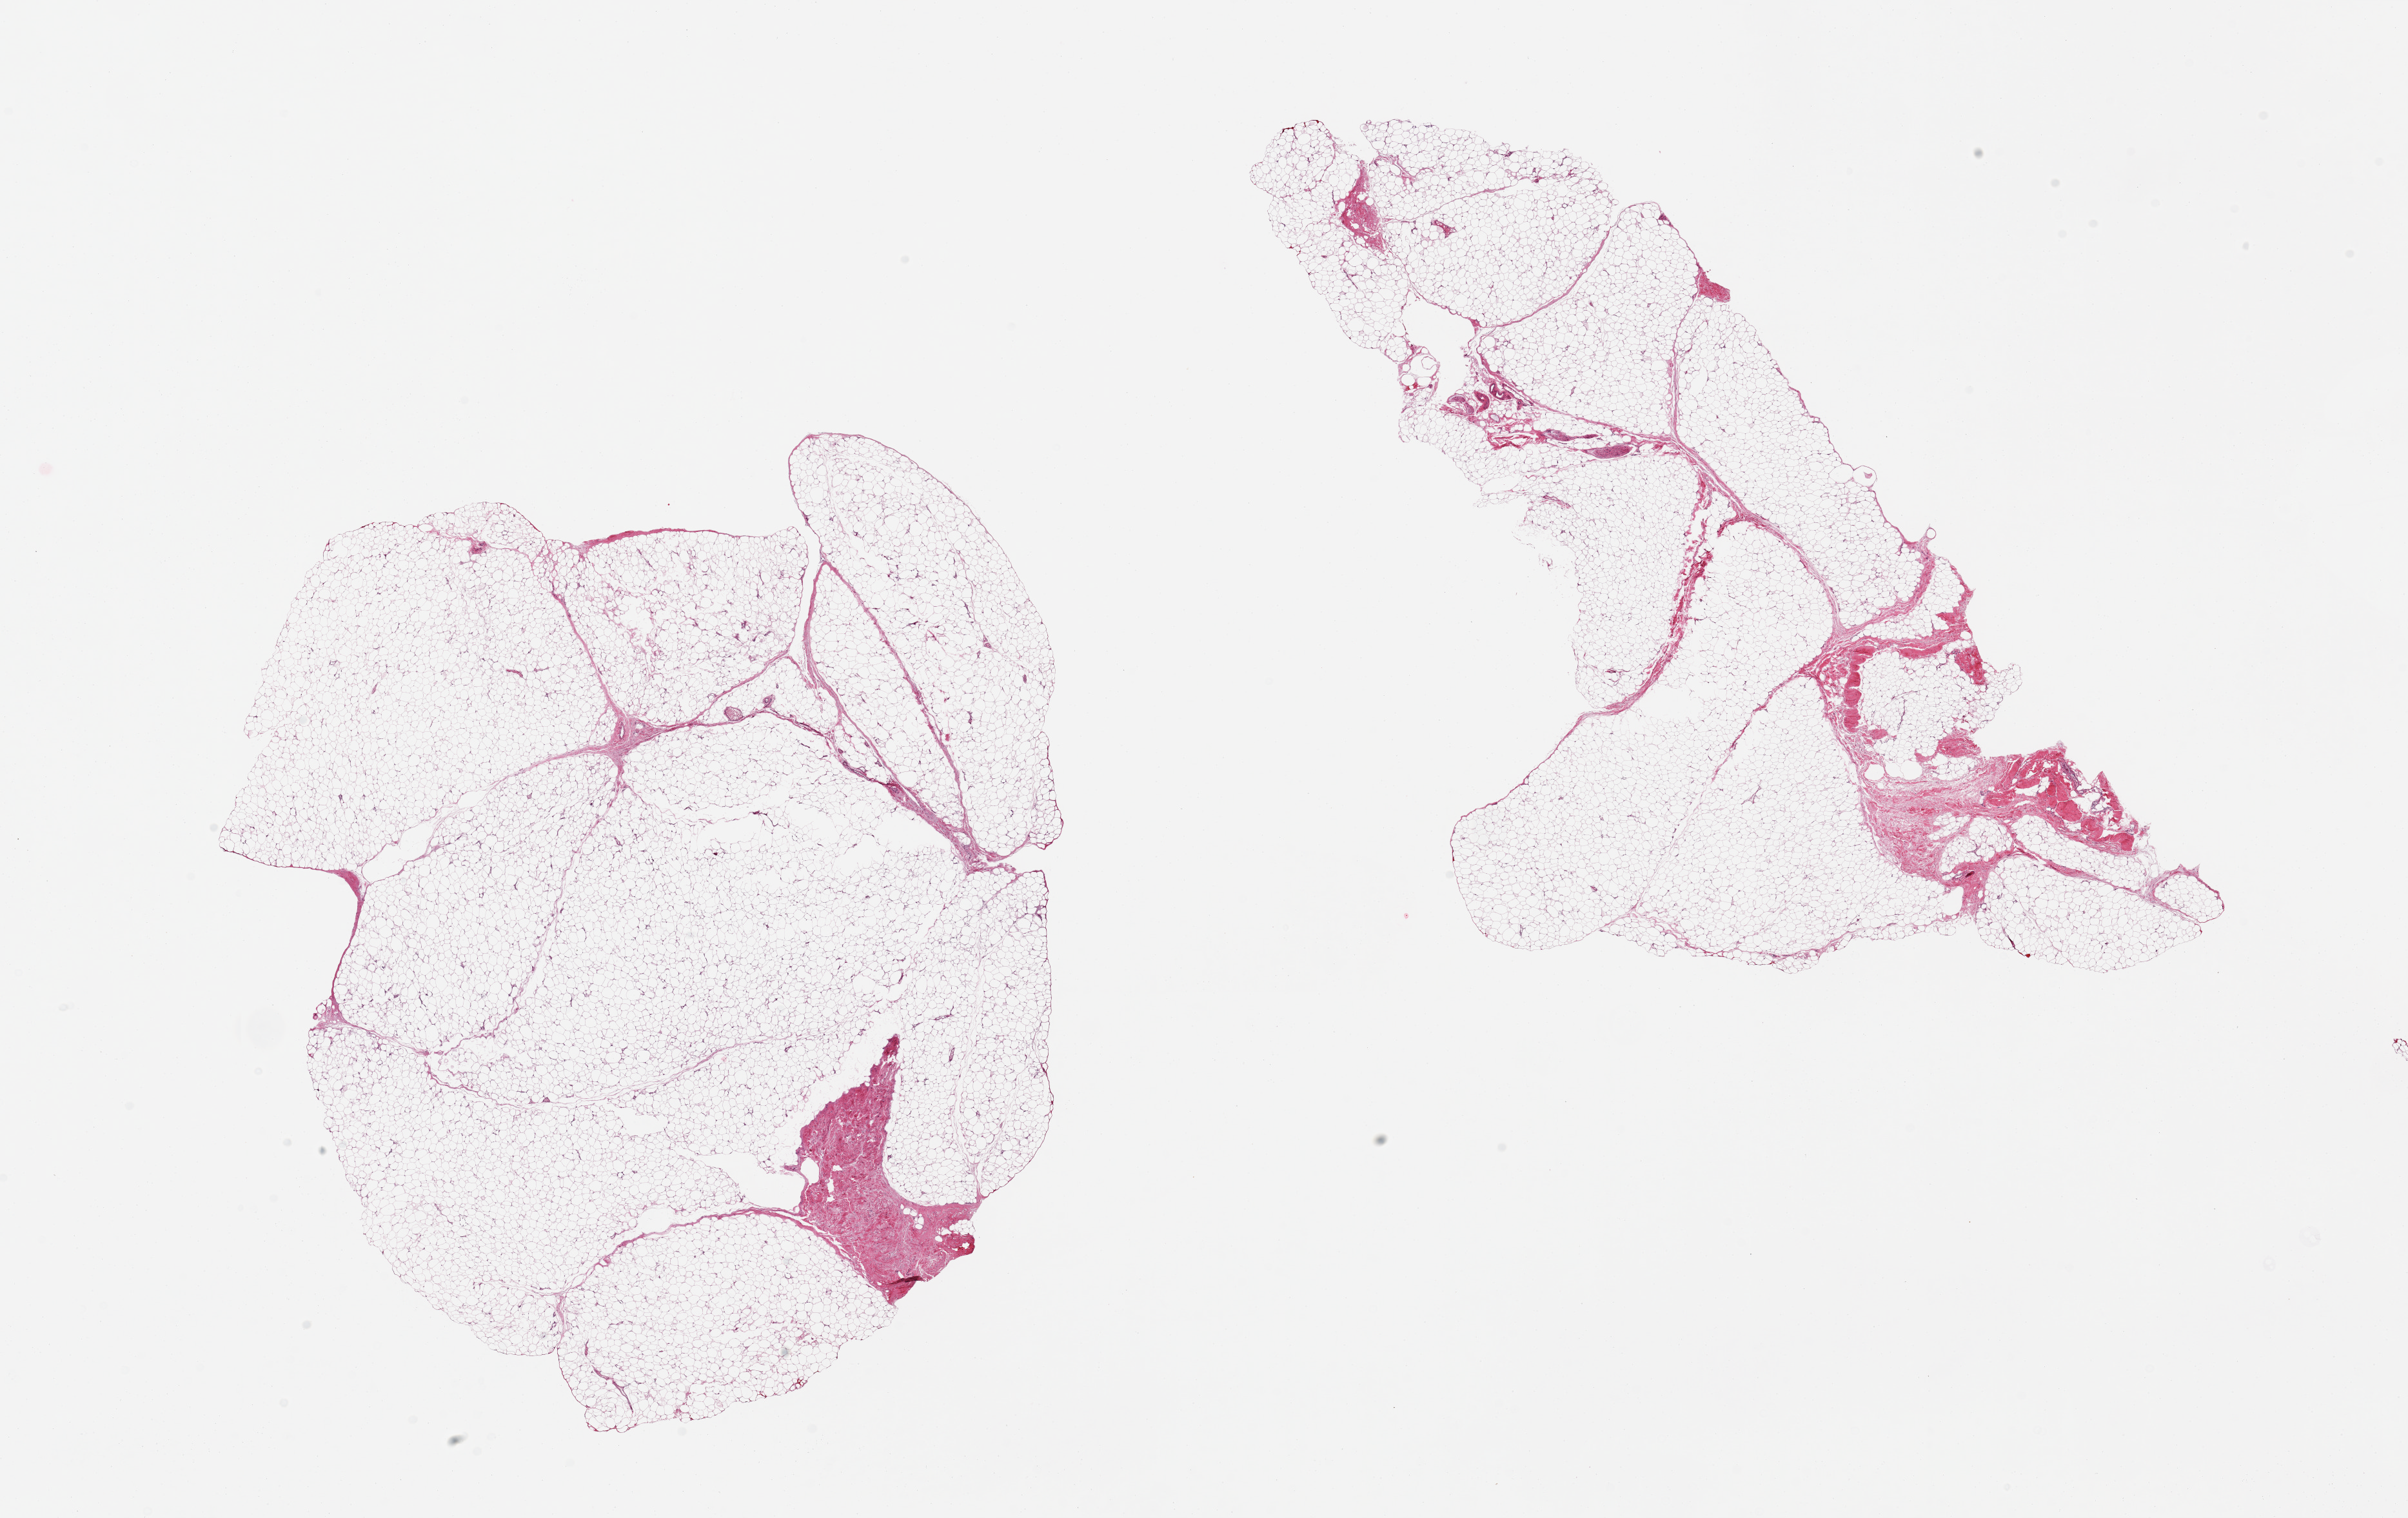
Whole-slide image, H&E stain, brightfield — low-resolution overview of the scanned area, about 29.5 x 18.6 mm (acquisition: 20x scan). PAXgene-fixed, paraffin-embedded tissue. Target tissue: adipose tissue. Donor tissue sample.
Review note (as recorded): 2 pieces, 12x11 & 15x7.5mm; ~19% fibrous tissue.